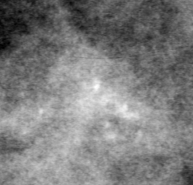
Crop from a digitized film mammogram around one marked abnormality; right breast; CC view.
- Marked abnormality: calcifications, morphology pleomorphic, distribution clustered; BI-RADS assessment category 4; subtlety rating 2 on a 1 (subtle) to 5 (obvious) scale; pathology result (as recorded, not read from the image): malignant.